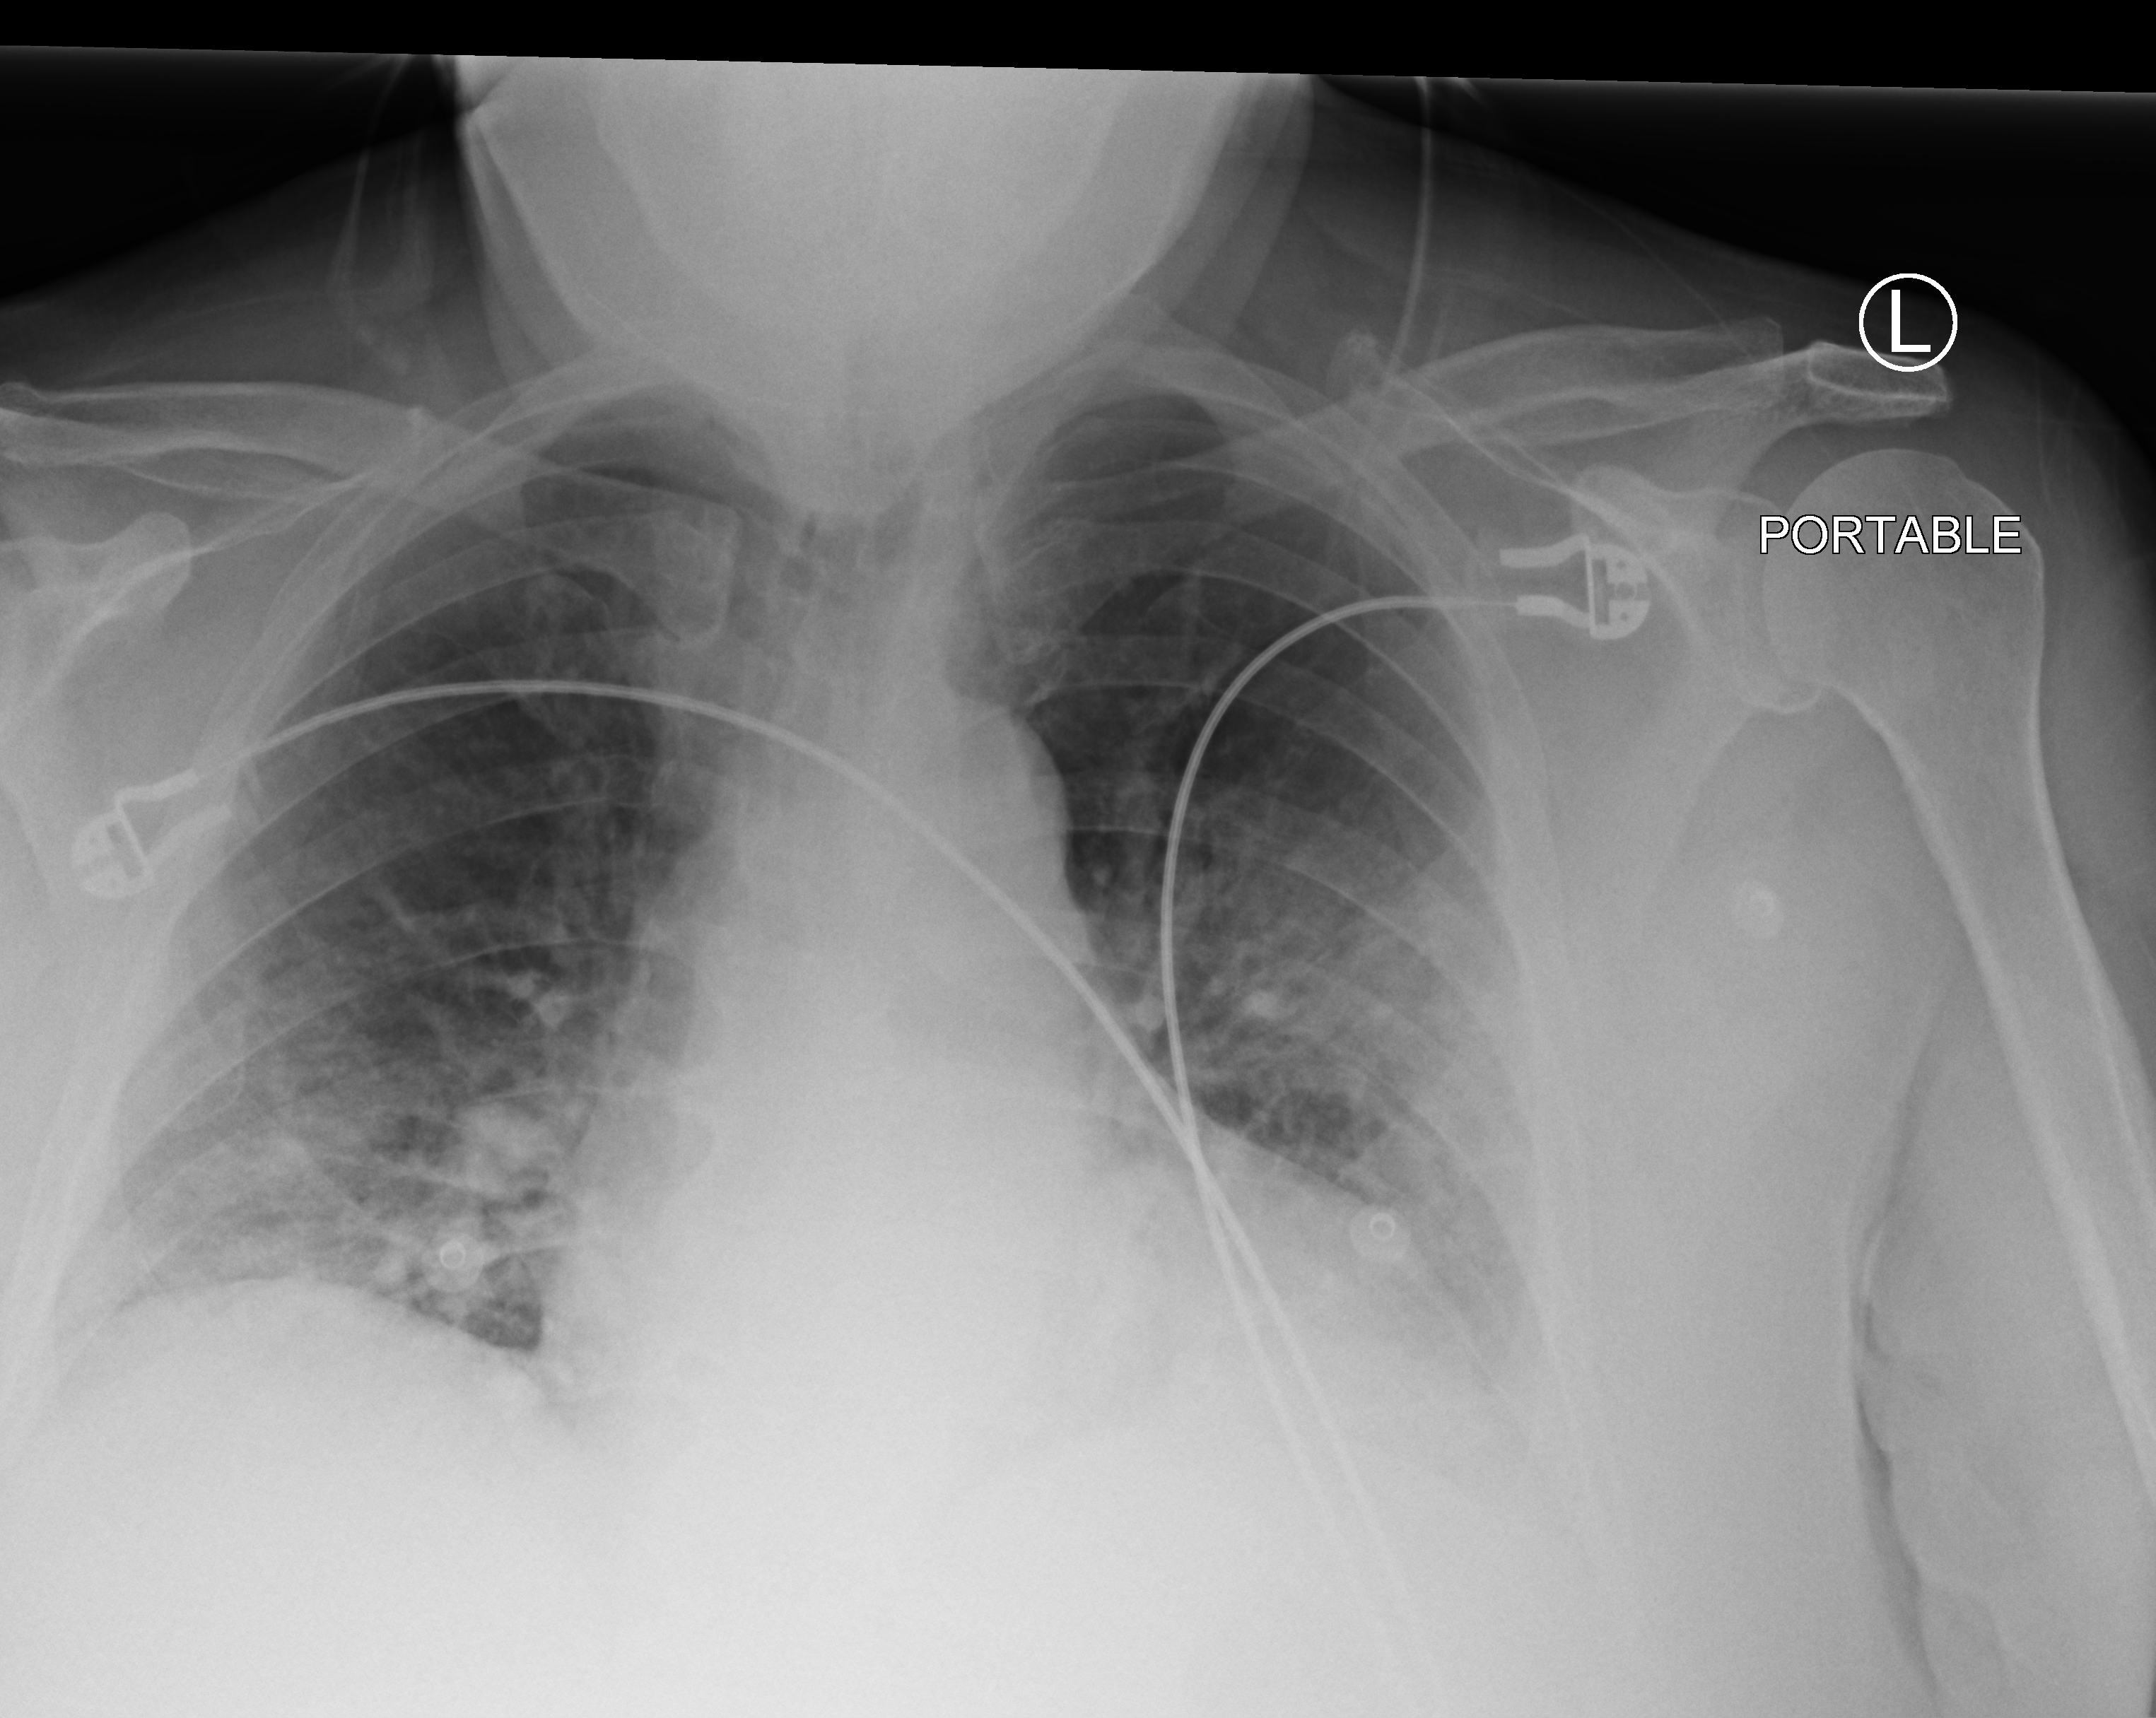
Chest X-ray (portable). Male patient hospitalised with COVID-19, age 60–74 years.
From the hospital-stay record, not from the radiograph (when in the stay this image was taken is not recorded):
- admitted to intensive care during this hospital stay: yes